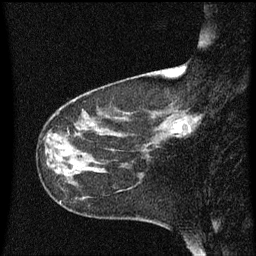
Breast MRI (dynamic contrast-enhanced), one sagittal slice; slice 20 of 60 in the series (ordered by position); dynamic contrast-enhanced series, image 2 of 3 at this slice position (ordered by acquisition); 1.5 T; TE 4.2 ms, TR 8.4 ms; 2 mm slice thickness; 256 × 256 image matrix, field of view 200 × 200 mm. Female patient, age 41 years. From the clinical record (not read from this slice): setting: breast cancer imaged before/during neoadjuvant chemotherapy; receptor status: triple-negative.
Structures marked on this image (semi-automatic segmentation, software-assisted and operator-edited):
- analysis volume of interest (the breast-tissue region the enhancement analysis was run in; not a lesion): box from (x=158, y=100) to (x=201, y=145) px
- tumour enhancement mask (voxels above the 70 % enhancement threshold inside the analysis volume of interest): (x=184, y=118)–(x=198, y=135)